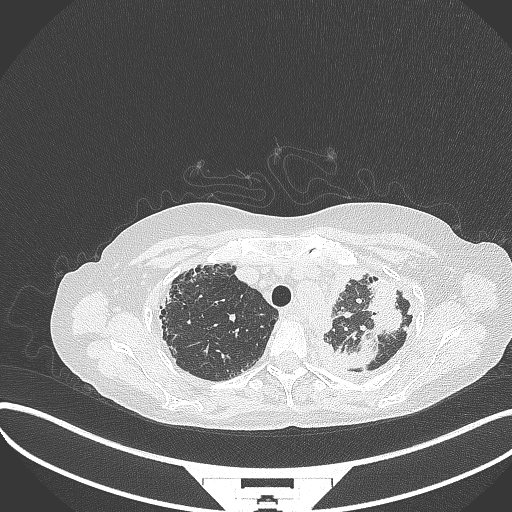
Chest CT, one axial slice; position 275 of 373 along the scan axis; lung window (W 1500 / L -600 HU); 1 mm slice thickness; 512 × 512 image matrix, field of view 400 × 400 mm. Patient: female, 56 years. From the clinical record (not read from this slice): clinical TNM (as recorded): T1 N0 M0.
Annotated regions visible in this slice (rectangle marked by the reading radiologist):
- lung tumour (recorded histology: adenocarcinoma): bounding box <337,277,406,370> (left, top, right, bottom; pixels)